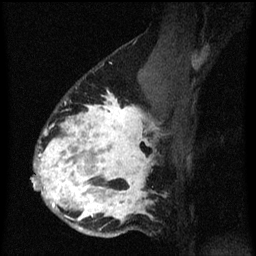
Breast MRI (dynamic contrast-enhanced), one sagittal slice. Dynamic contrast-enhanced series, image 2 of 3 at this slice position (ordered by acquisition). 1.5 T. TE 4.2 ms, TR 8.4 ms. 256 × 256 image matrix, field of view 180 × 180 mm. Patient: female, 34 years. From the clinical record (not read from this slice): setting: breast cancer imaged before/during neoadjuvant chemotherapy; receptor status: HR-positive, HER2-negative.
Annotated regions visible in this slice (semi-automatic segmentation, software-assisted and operator-edited):
- analysis volume of interest (the breast-tissue region the enhancement analysis was run in; not a lesion): box from (x=32, y=58) to (x=171, y=239) px
- tumour enhancement mask (voxels above the 70 % enhancement threshold inside the analysis volume of interest): (x=32, y=94)–(x=157, y=223)